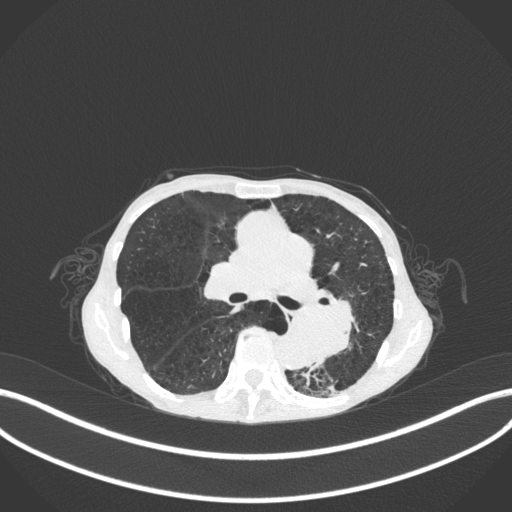
Chest CT, one axial slice. Position 162 of 347 along the scan axis. 120 kVp. Lung window (W 1500 / L -600 HU). 1 mm slice thickness. 512 × 512 image matrix, field of view 400 × 400 mm. Female patient, age 70 years. Case-level facts recorded for this patient, not image findings: clinical TNM (as recorded): T3 N0 M0; histopathological grade: G3.
Annotated regions visible in this slice (bounding box drawn by a radiologist):
- lung tumour (recorded histology: small cell carcinoma): bounding box <305,283,369,368> (left, top, right, bottom; pixels)